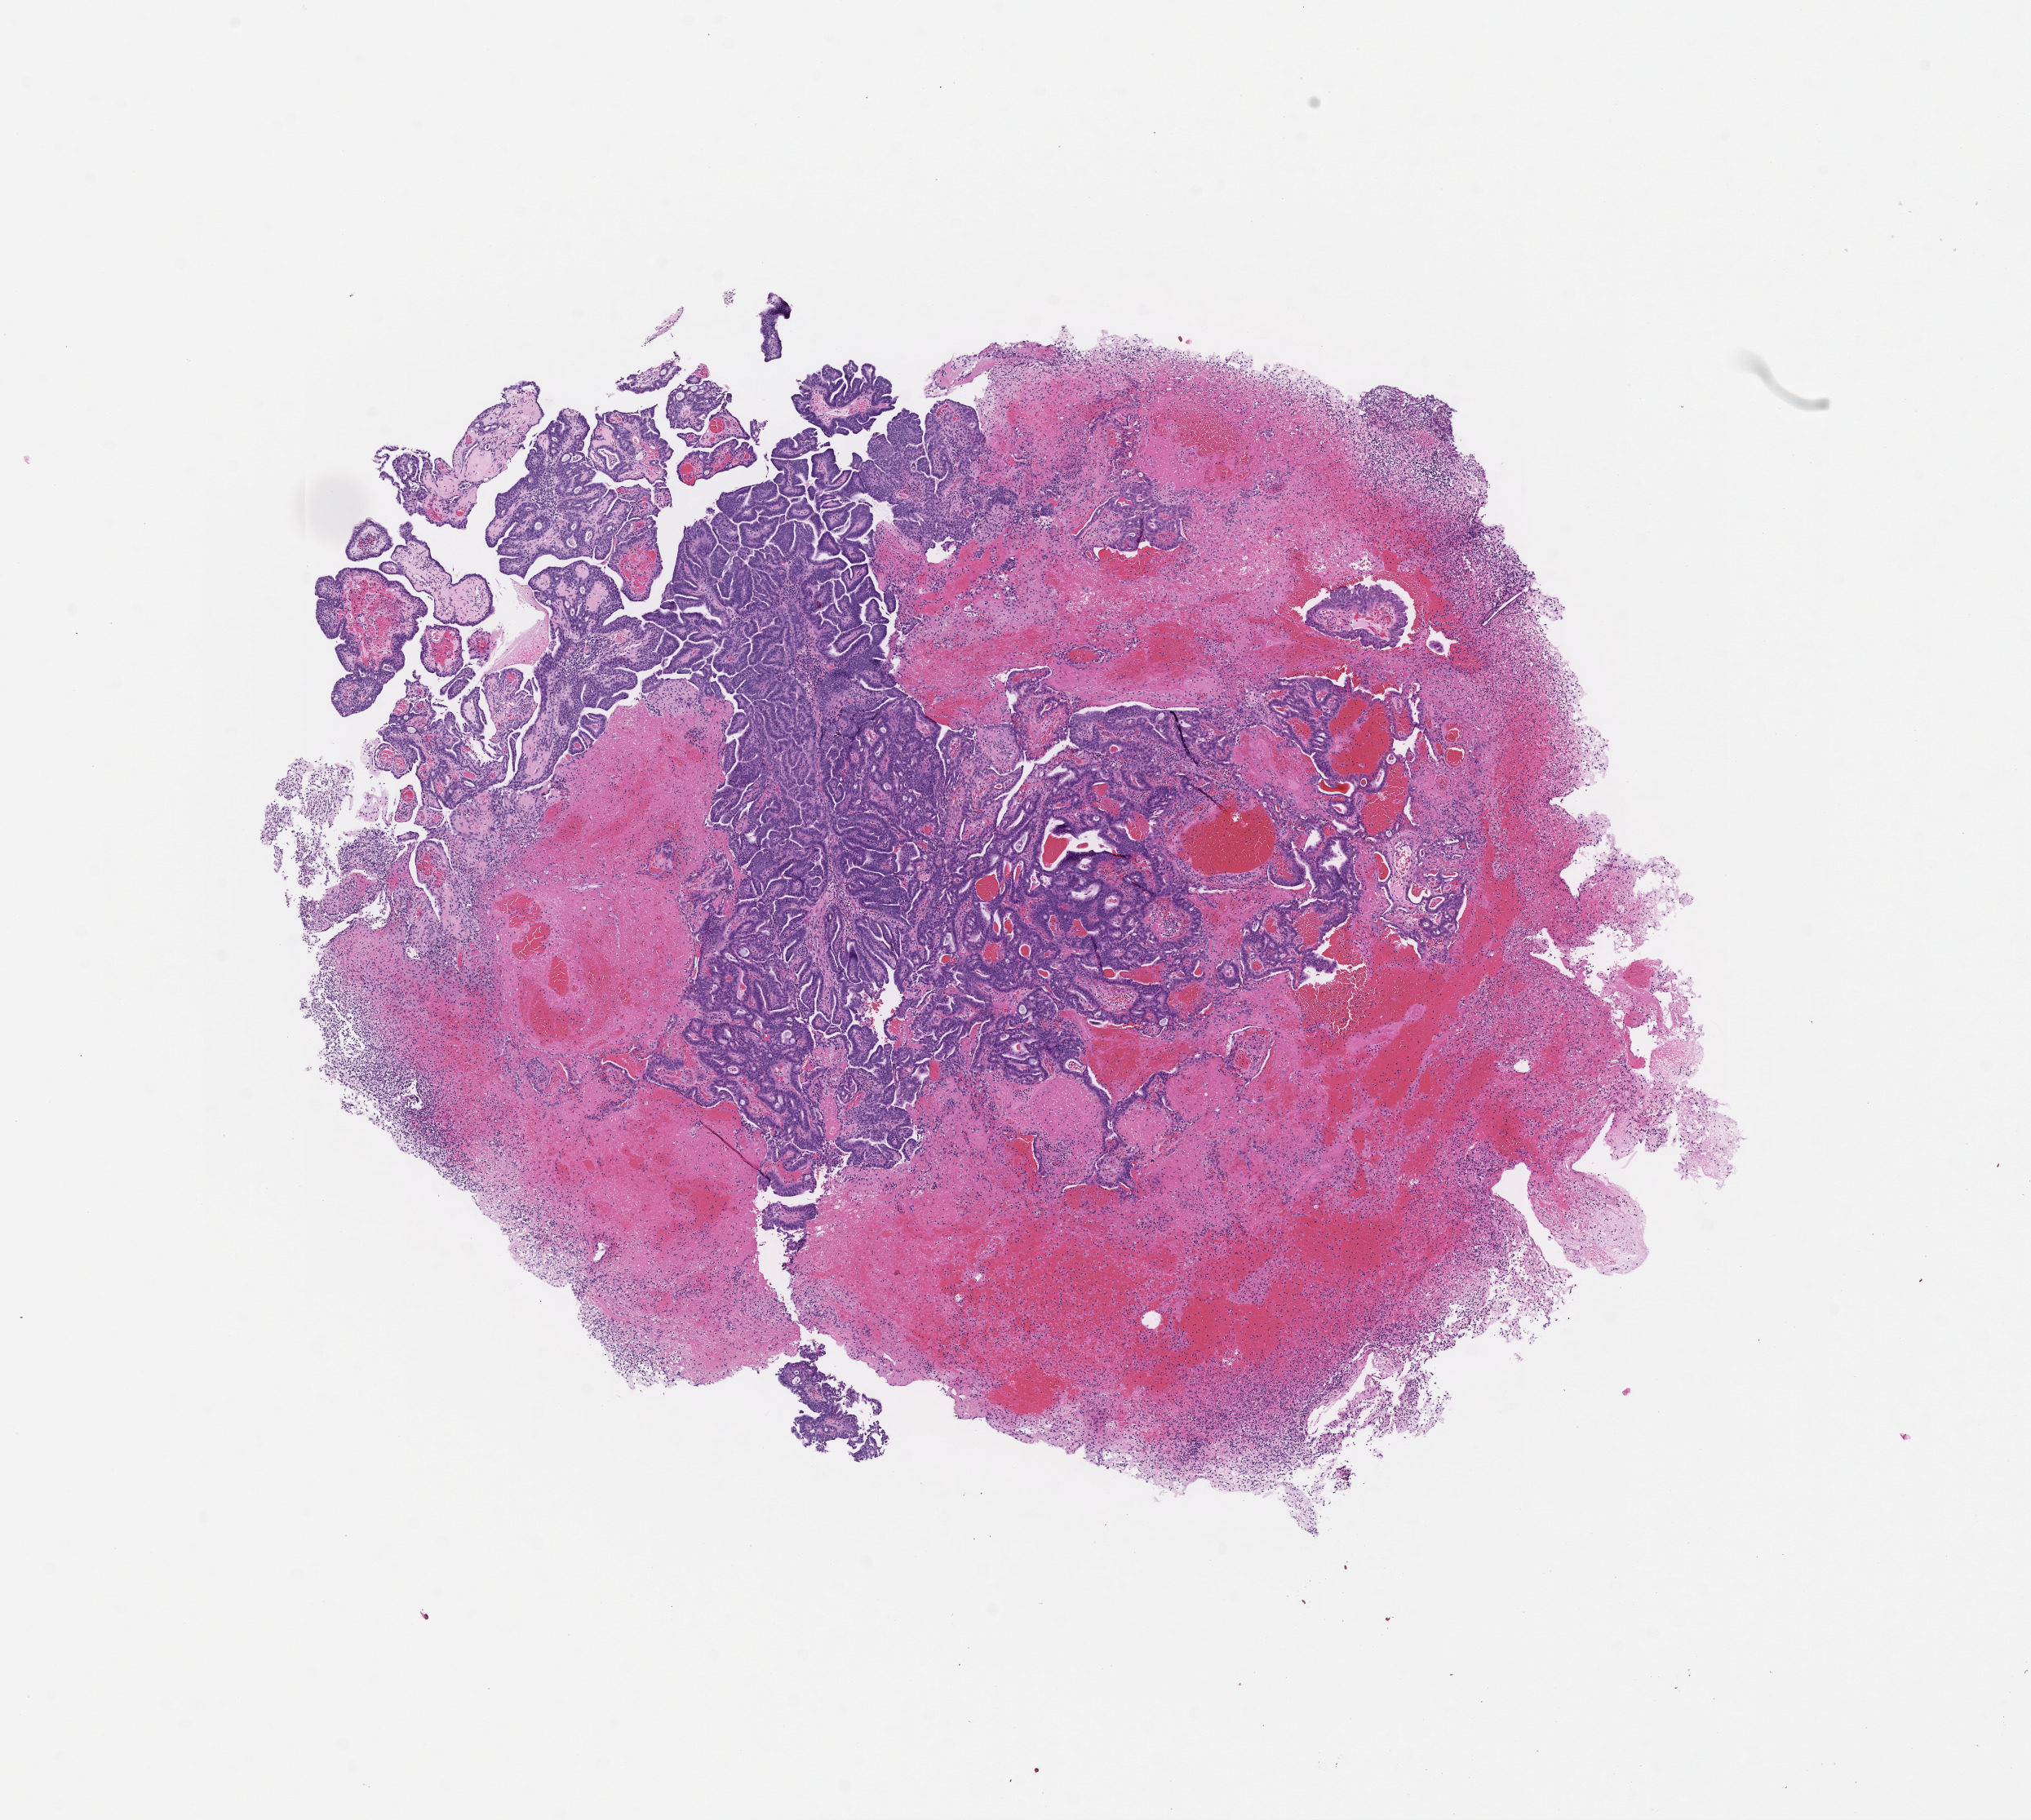
H&E whole-slide image — low-resolution overview of the scanned area, about 10.1 x 9.0 mm, formalin-fixed paraffin-embedded section, specimen time point: collected at disease progression. Female patient.
- this section: metastasis (sampled organ not recorded)
- primary diagnosis of the patient: Colorectal Carcinoma